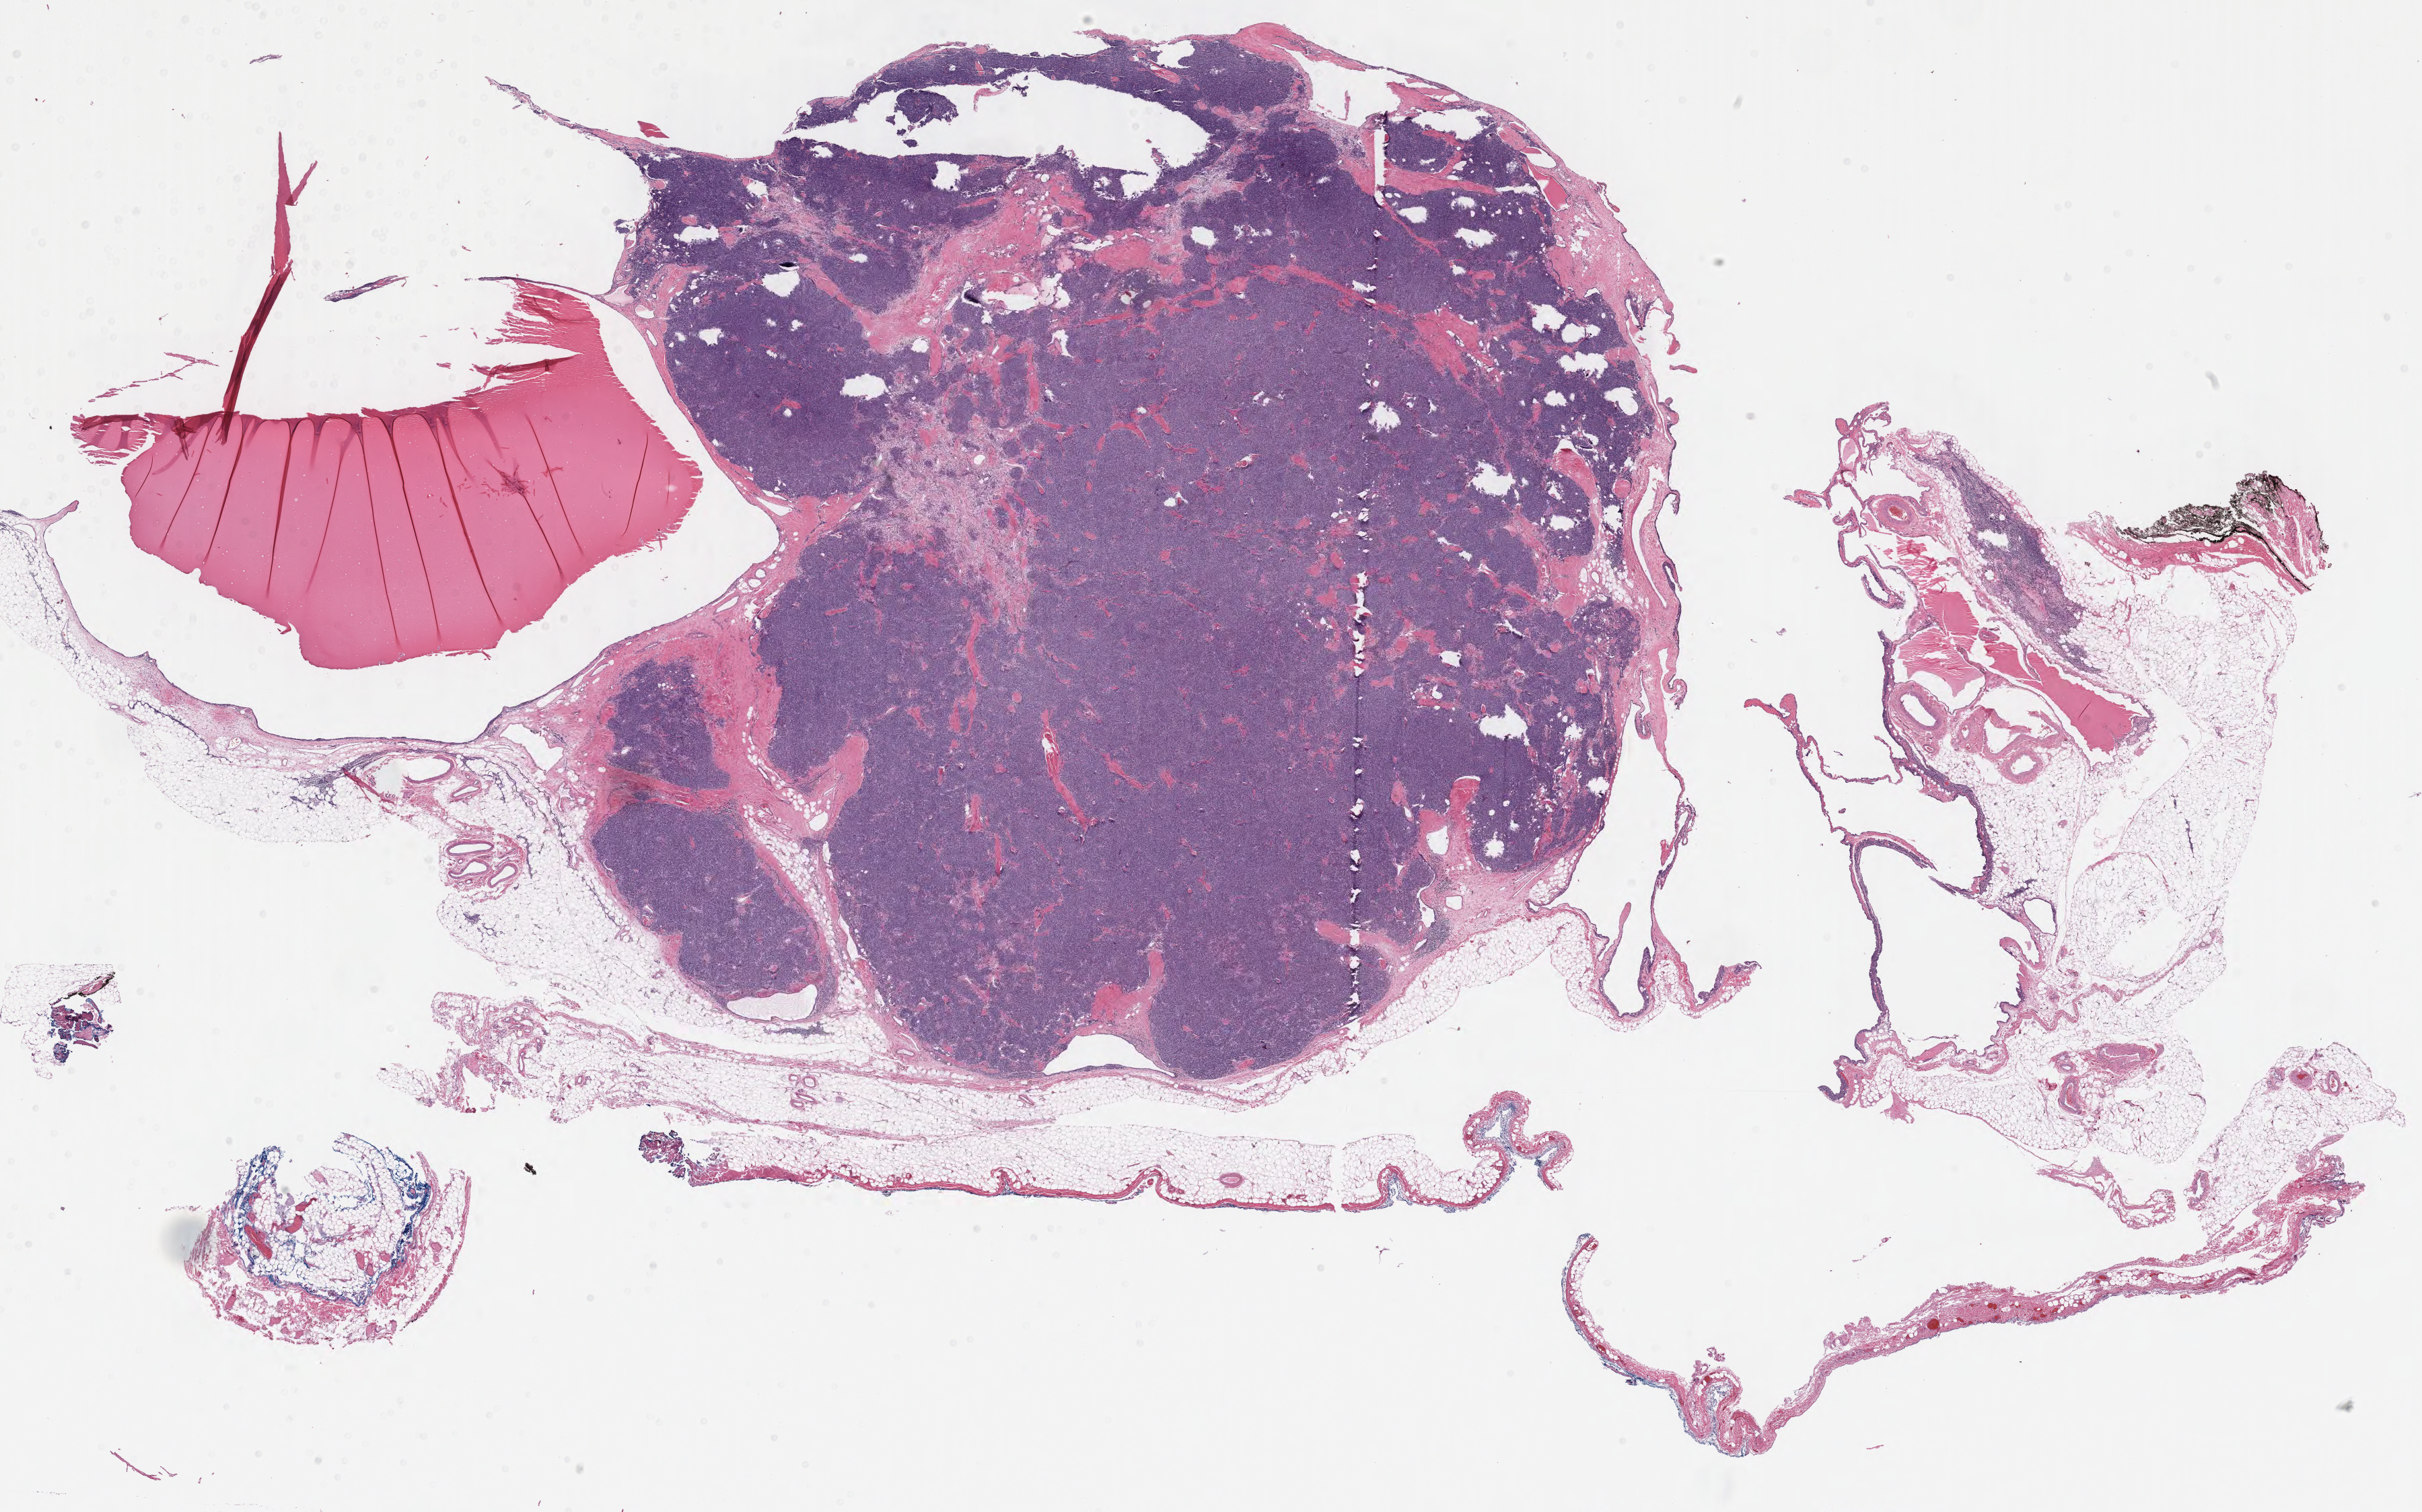
Whole-slide histology image, H&E, a low-resolution overview of the entire scanned area, about 28.5 x 17.8 mm (acquisition: 40x scan); formalin-fixed paraffin-embedded (FFPE) diagnostic section; primary tumour sample from the thymus. Male, age 52 years at initial diagnosis.
Pathologic diagnosis: Thymoma, type A, malignant.